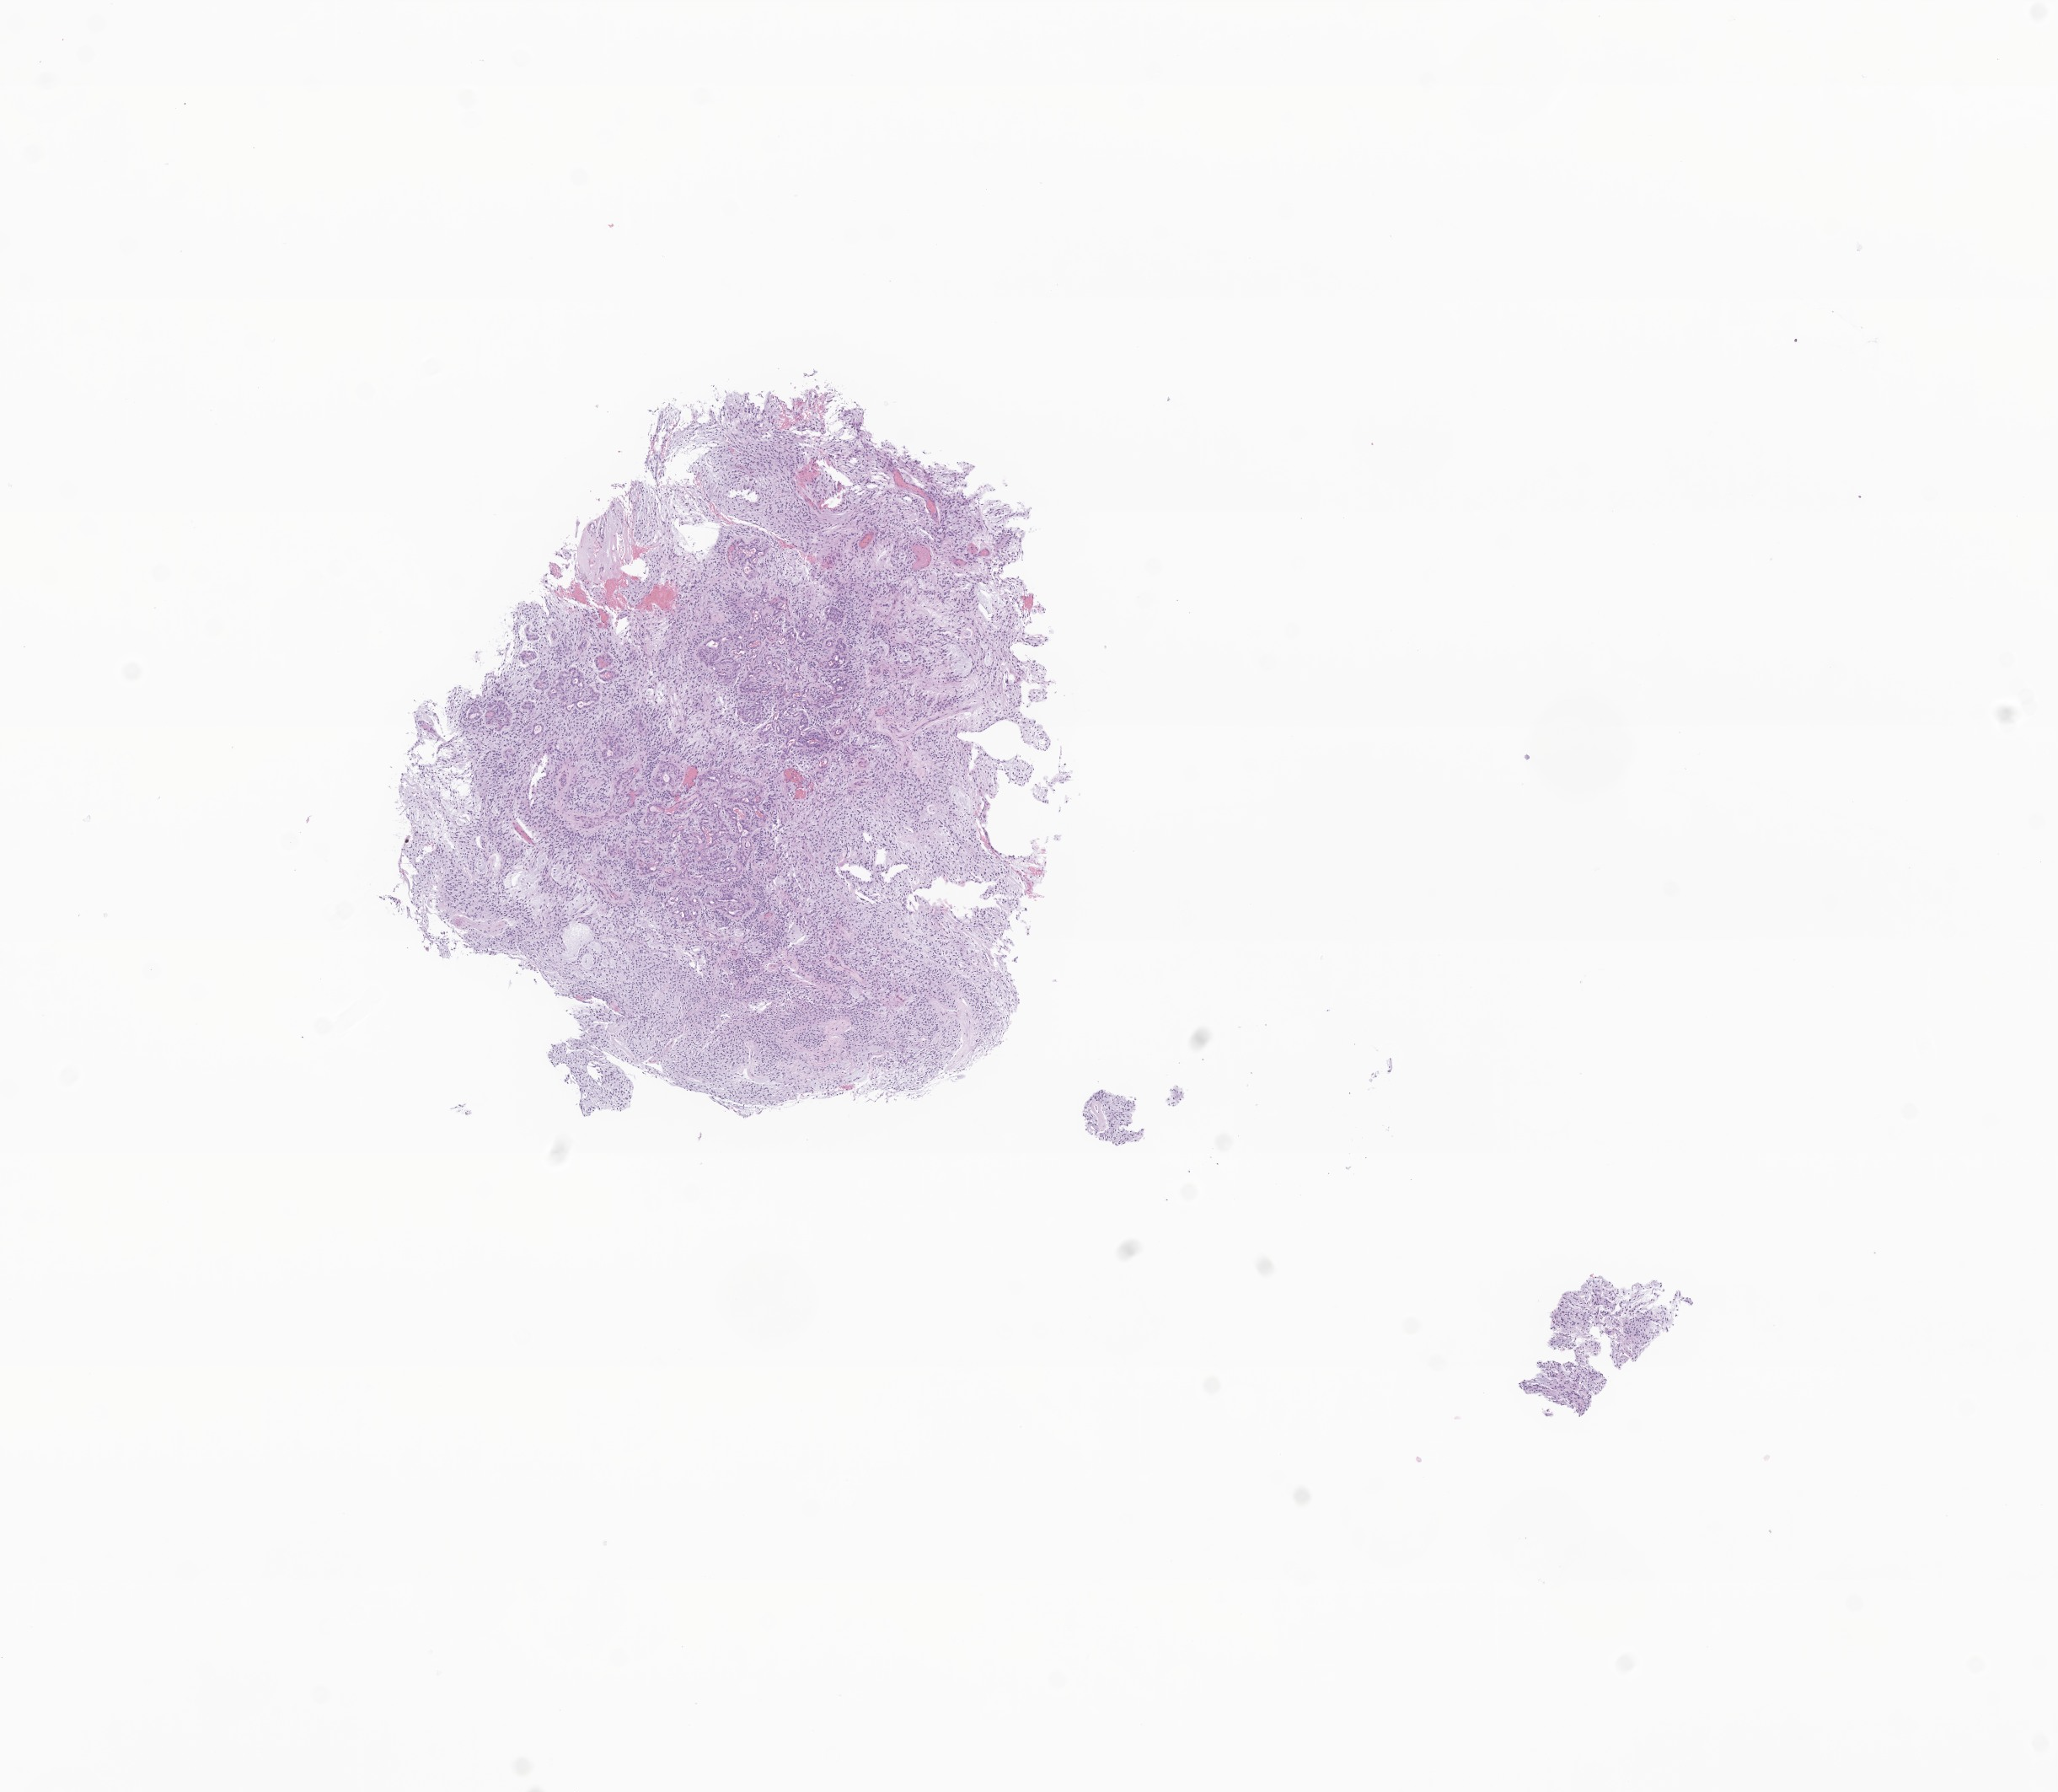
H&E whole-slide image of tumor tissue from the spinal cord, low-resolution overview of the scanned area, about 10.3 x 9.0 mm, formalin-fixed paraffin-embedded section. Female patient, age 40 months (3 years 4 months).
* diagnosis (ICD-O-3 morphology term): Pilocytic astrocytoma